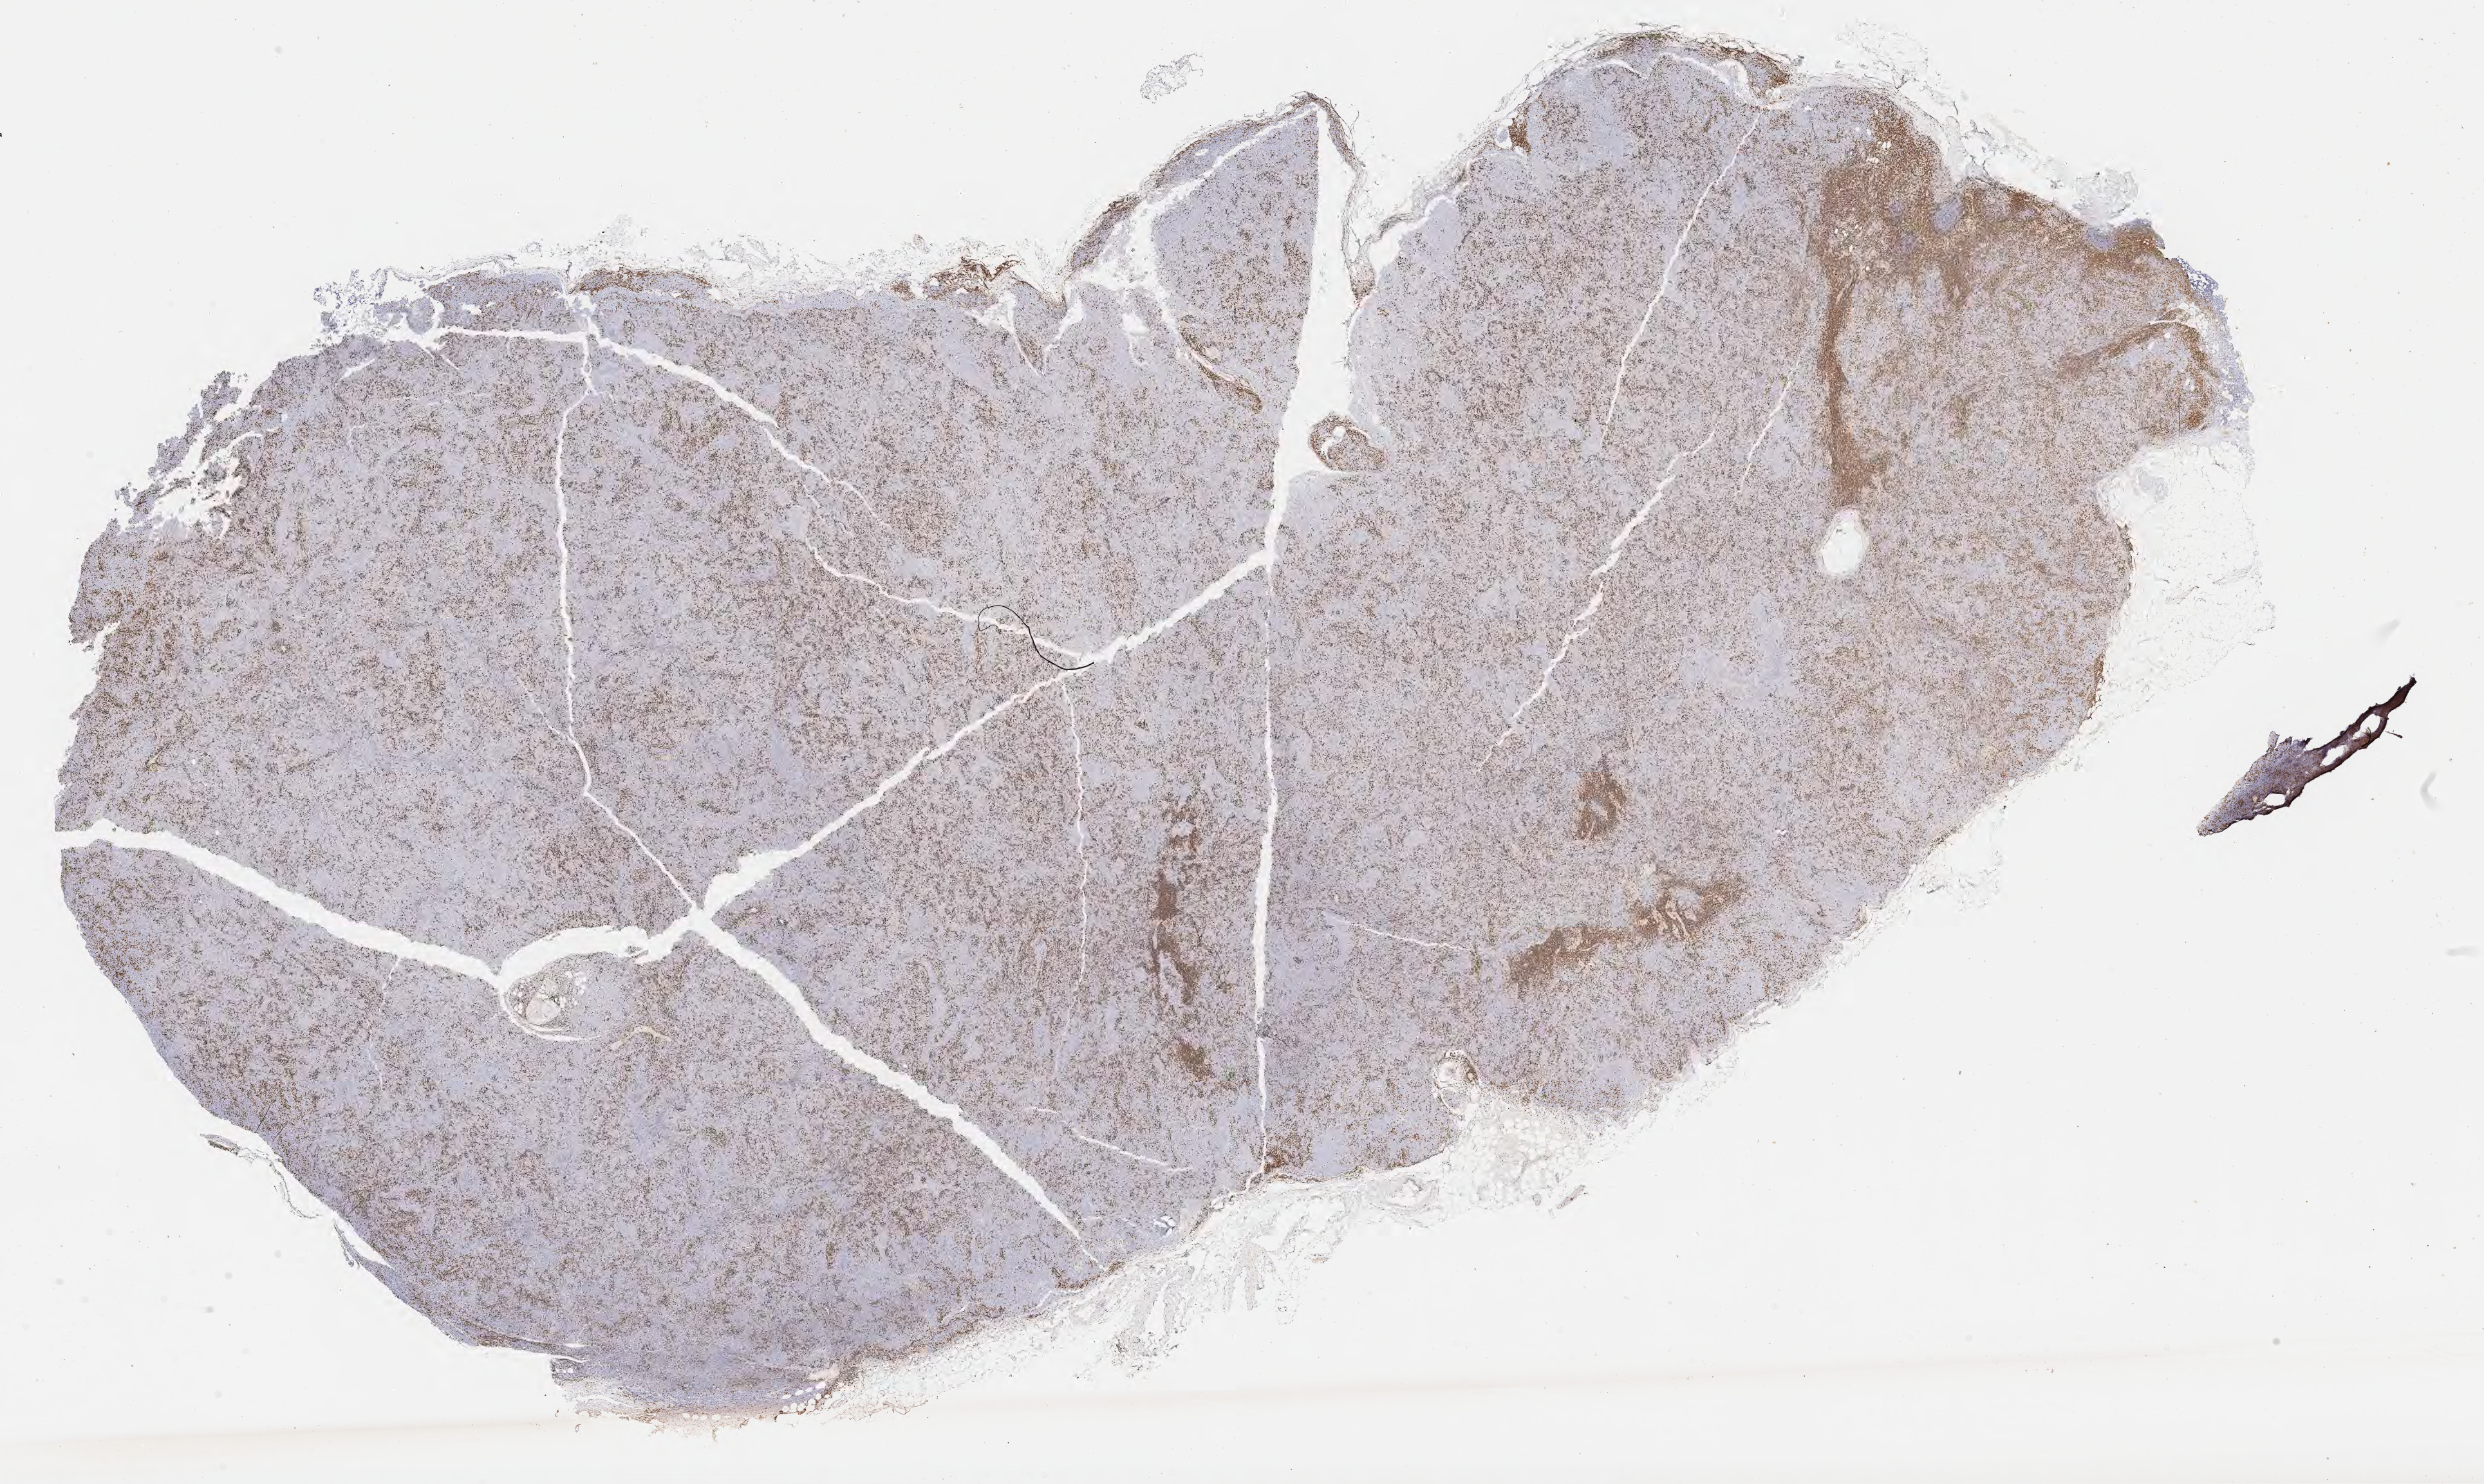
Whole-slide image, immunohistochemical stain for CD3 — shown as a low-resolution overview of the whole scanned area (about 31.2 x 18.6 mm). Tumor tissue. Male patient, 69 years old.
Diagnosis: Diffuse large B-cell lymphoma, NOS.